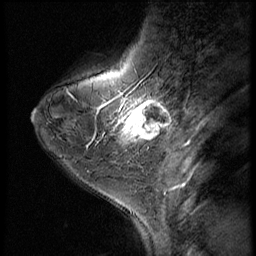
Breast MRI (dynamic contrast-enhanced), one sagittal slice; slice 17 of 56 in the series (ordered by position); dynamic contrast-enhanced series, image 2 of 3 at this slice position (ordered by acquisition); 1.5 T; TE 4.2 ms, TR 9 ms; 2.5 mm slice thickness; 256 × 256 image matrix, field of view 180 × 180 mm. Female patient, age 38 years. From the clinical record (not read from this slice): setting: breast cancer imaged before/during neoadjuvant chemotherapy; receptor status: triple-negative.
Outlined on this slice (semi-automatically segmented with operator editing):
- analysis volume of interest (the breast-tissue region the enhancement analysis was run in; not a lesion): bounding box <107,95,176,149> (left, top, right, bottom; pixels)
- tumour enhancement mask (voxels above the 140 % enhancement threshold inside the analysis volume of interest): <114,98,170,141>